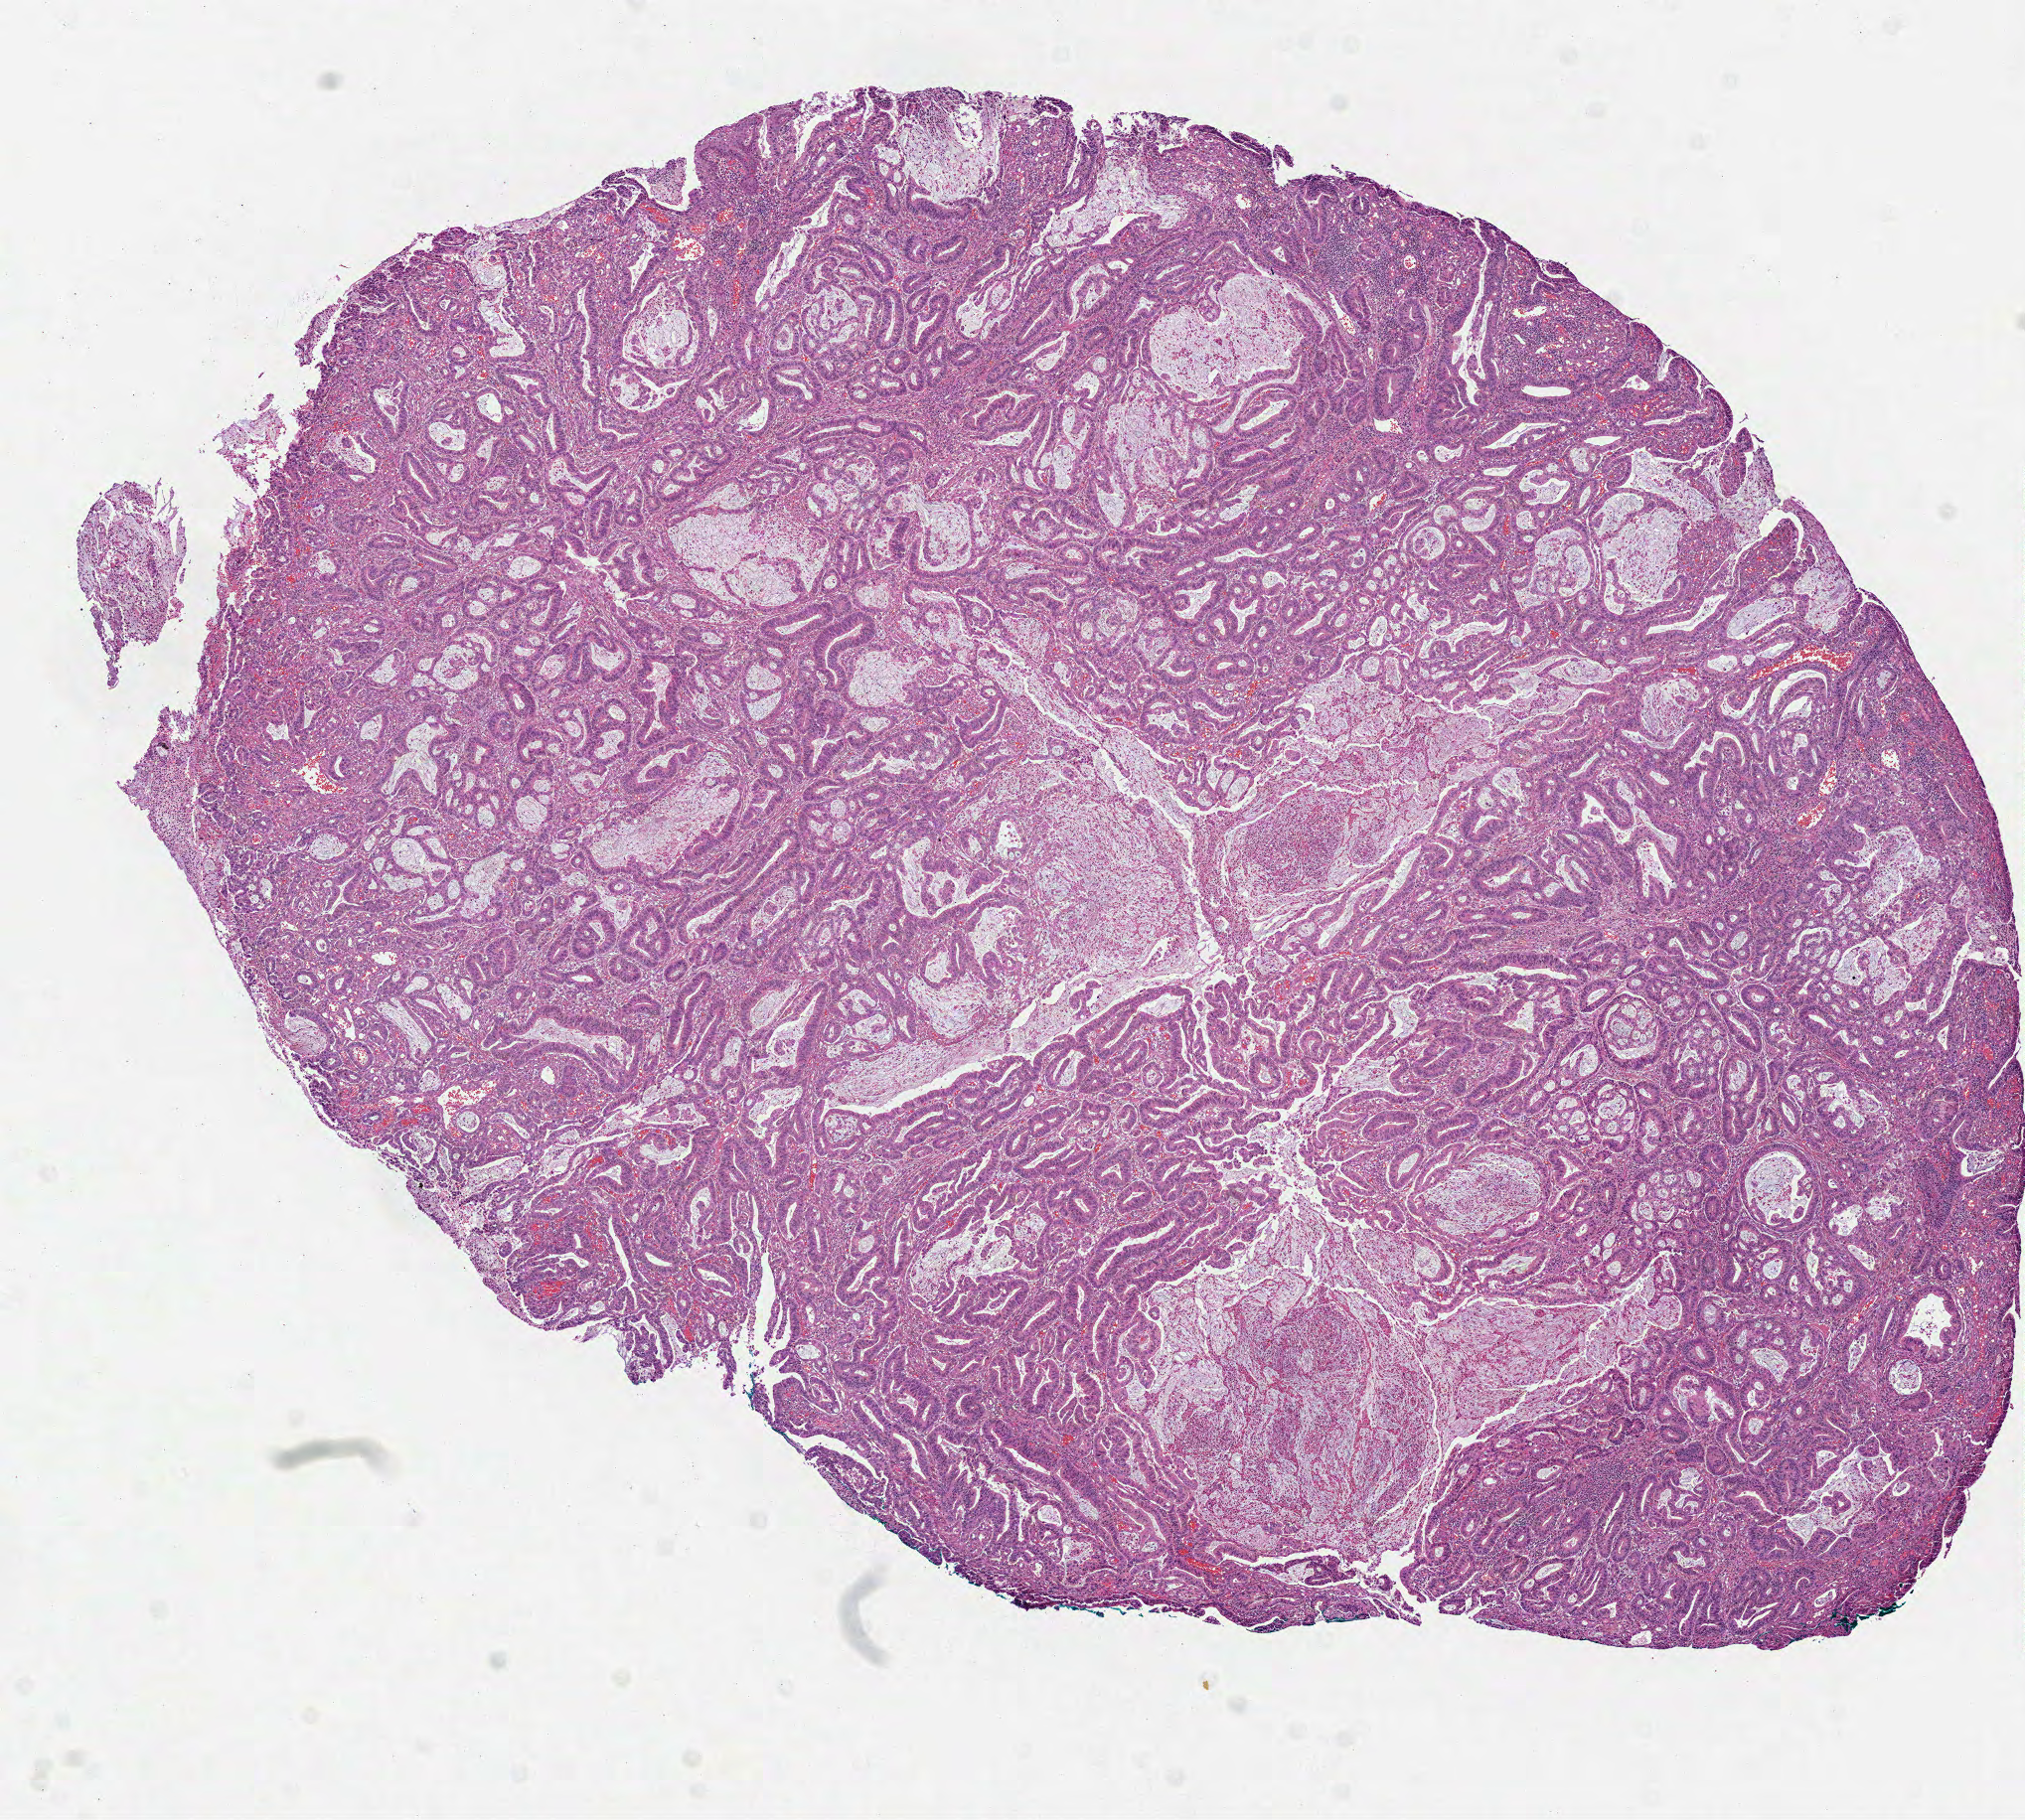
Digitized H&E-stained tissue section (whole slide) — whole scanned area (about 8.2 x 7.4 mm, from a 40x scan) shown as a low-resolution overview, FFPE section, primary tumour sample from the stomach. Male, age 69 years at initial diagnosis. Histologic grade: G2 (moderately differentiated).
* lymph nodes positive (case pathology): 2 of 17 examined
* AJCC pathologic stage: IIB (7th edition)
* histologic diagnosis: Mucinous adenocarcinoma (cardia, NOS)